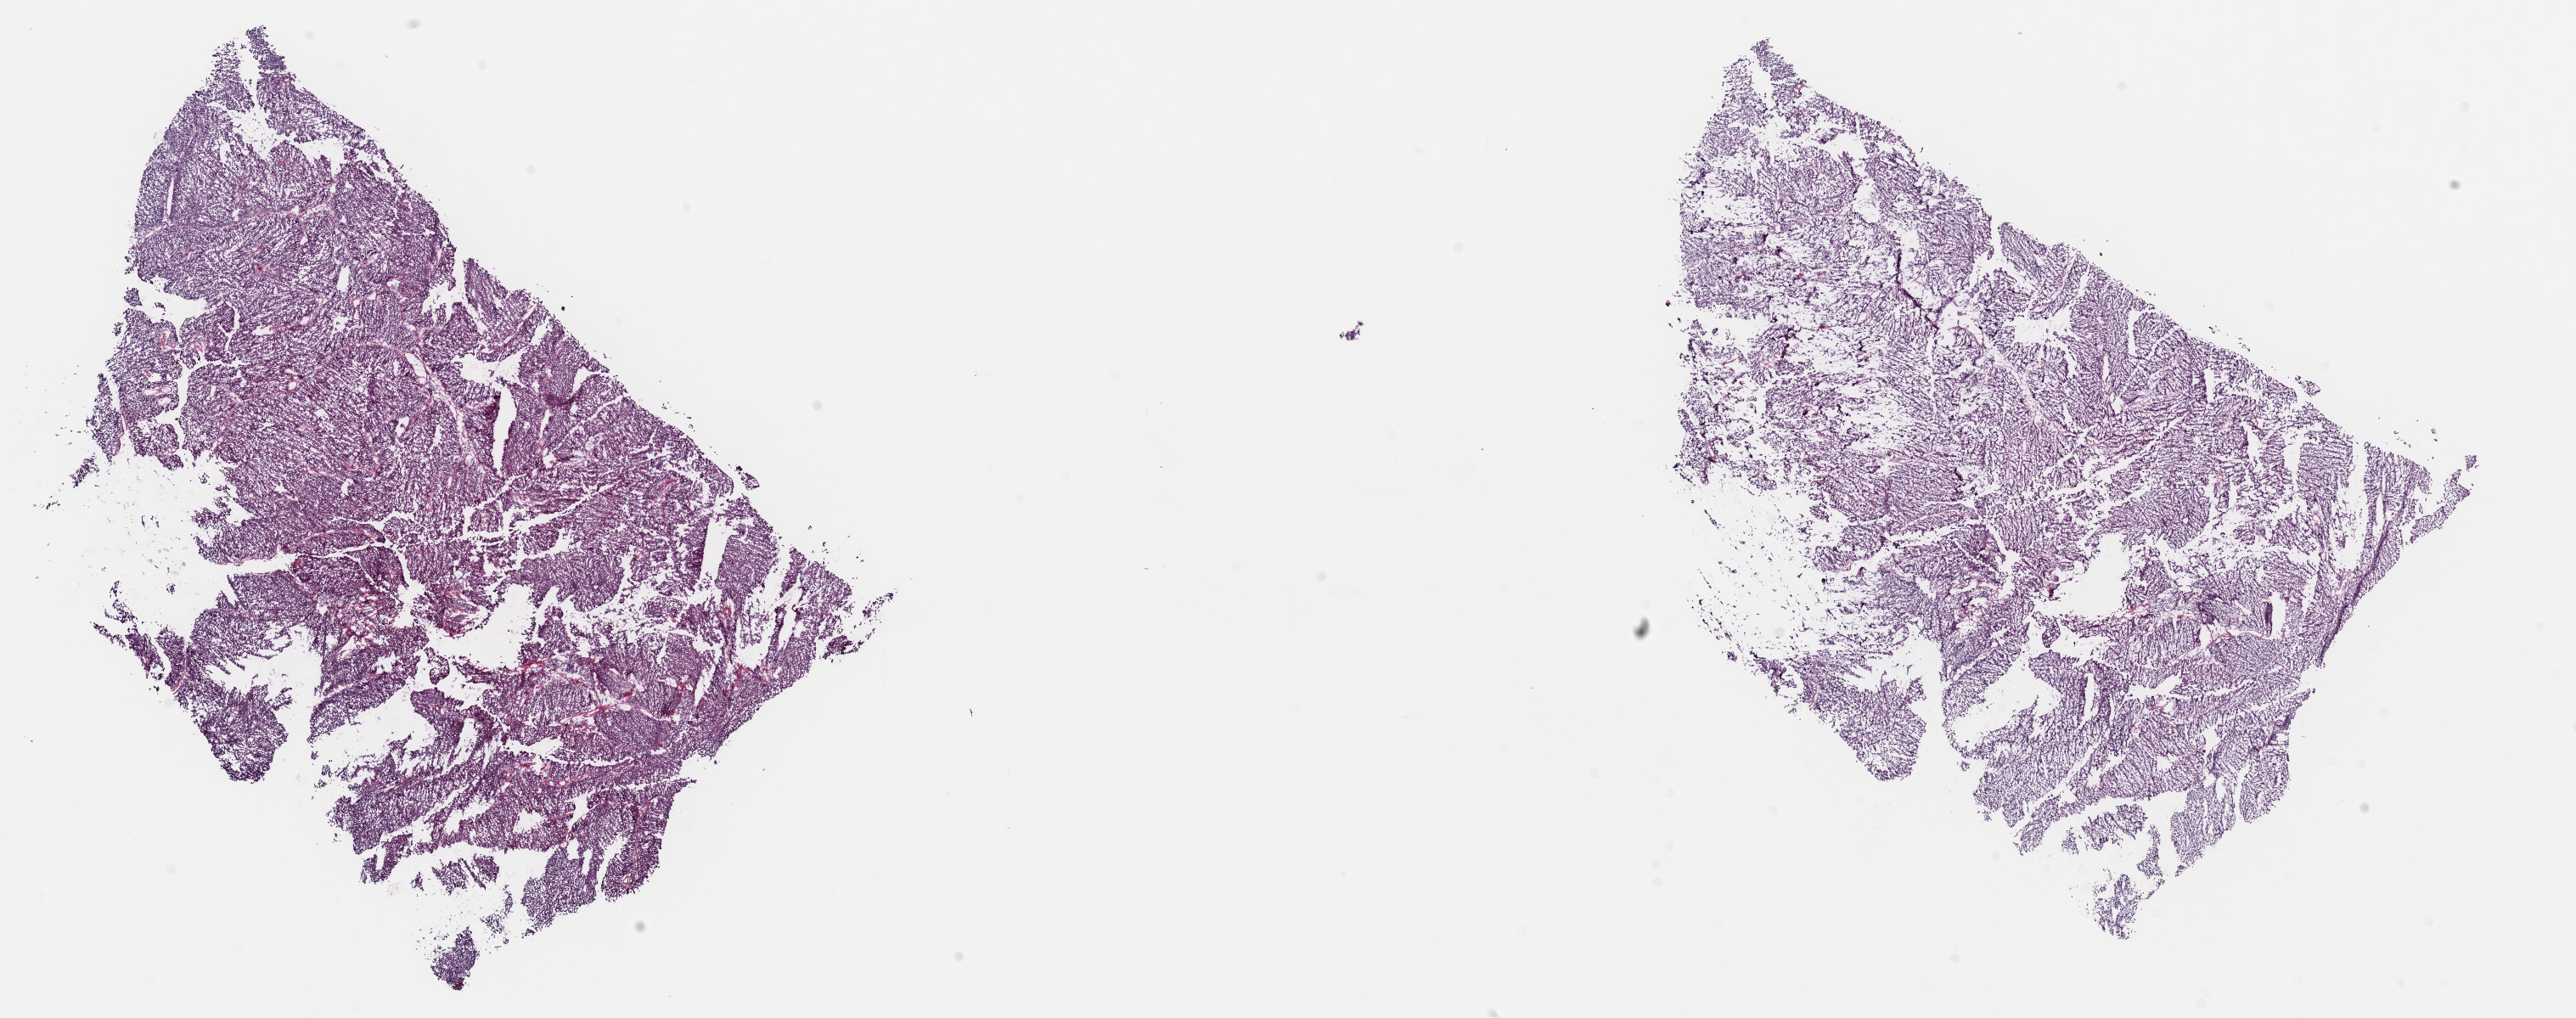
Whole-slide histology image, H&E-stained — low-resolution overview of the scanned area, about 24.0 x 9.5 mm, frozen section from the top of the tissue portion, bladder, primary tumour sample. Male patient; age at initial diagnosis 55 years. Histologic grade: low grade. Slide review estimates, as recorded: tumour cells 85%, tumour nuclei 95%, normal cells 0%, stromal cells 14%, necrosis 1%. Infiltration values recorded for this section: lymphocyte infiltration 1%, monocyte infiltration 0%, neutrophil infiltration 0%.
TNM: T3 N0 M0. AJCC pathologic stage: III (7th edition). Pathologic diagnosis: Transitional cell carcinoma.